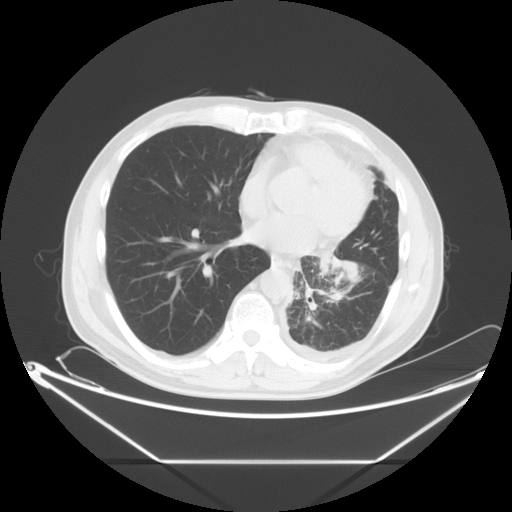
Chest CT, one axial slice; position 27 of 63 along the scan axis; reconstruction kernel STANDARD; 120 kVp; lung window (W 1500 / L -600 HU); 5 mm slice thickness; 512 × 512 image matrix. Patient: male, 60 years. Case-level facts recorded for this patient, not image findings: clinical TNM (as recorded): T4 N1 M1.
Structures marked on this image (rectangle marked by the reading radiologist):
- lung tumour (recorded histology: adenocarcinoma): bounding box <308,248,360,292> (left, top, right, bottom; pixels)